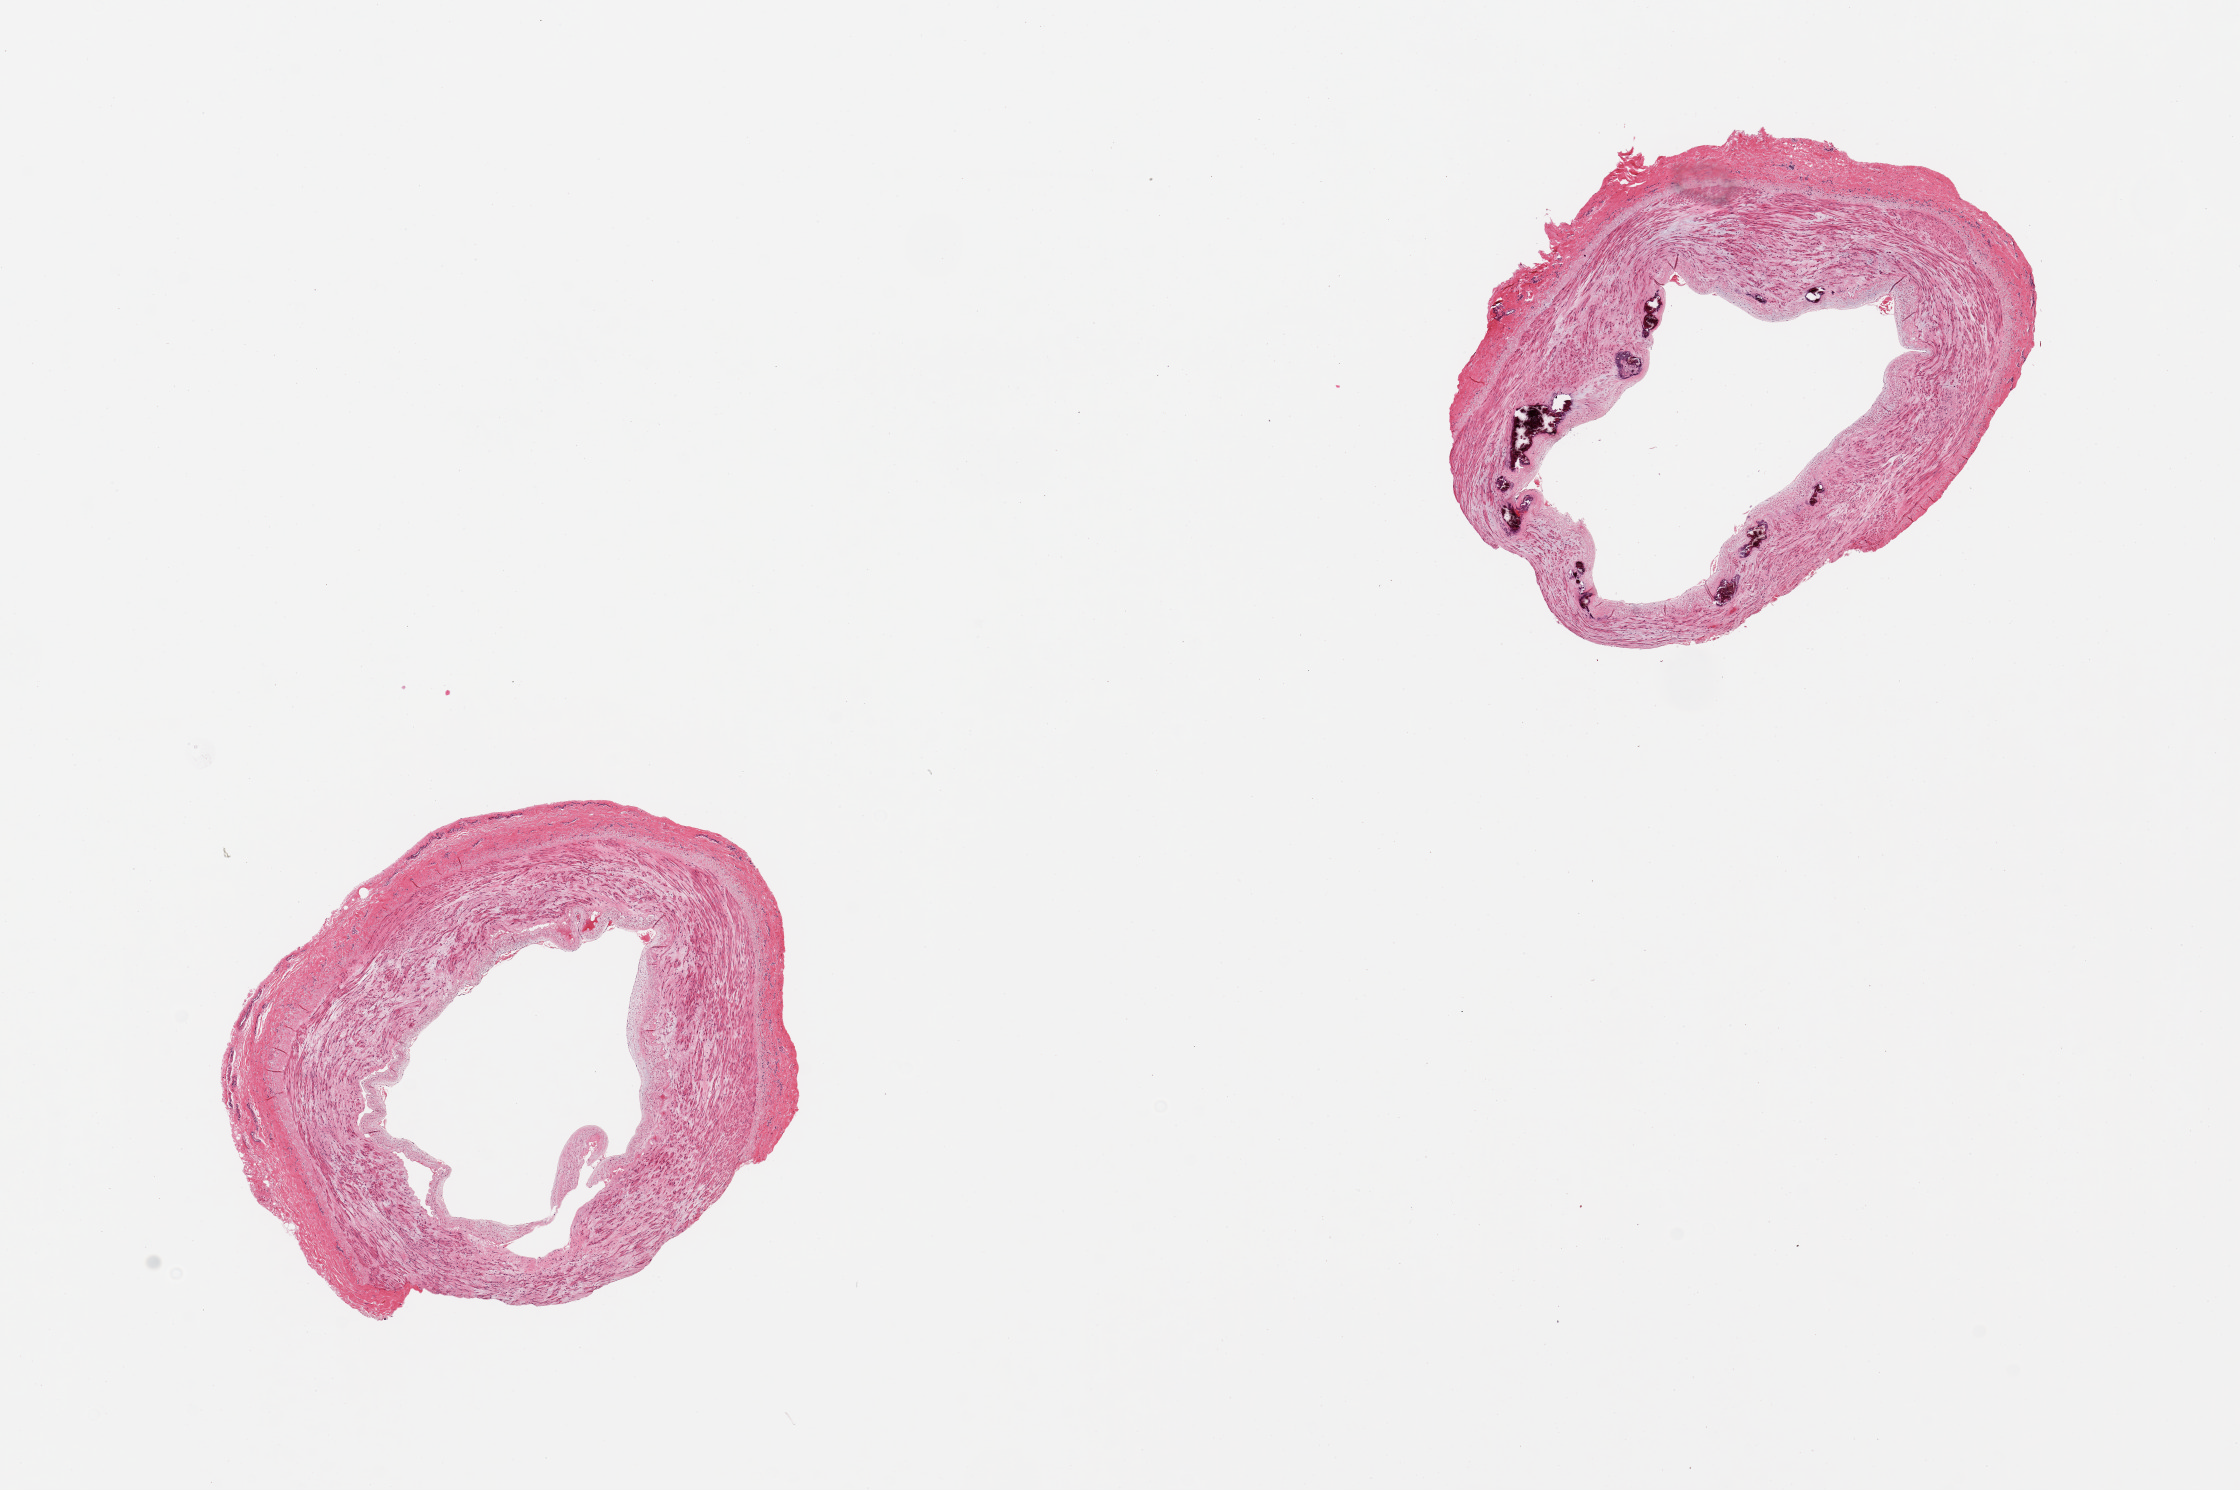
Whole-slide image, hematoxylin and eosin (H&E) stain, whole scanned area (about 17.7 x 11.8 mm, from a 20x scan) shown as a low-resolution overview. PAXgene-fixed paraffin-embedded (PFPE) section. Sampled site (target tissue): tibial artery. Tissue donor sample. Donor sex: female.
Reviewer comment on this tissue sample: 2 pieces, foci of Monckeberg's sclerosis; Good clean specimens.